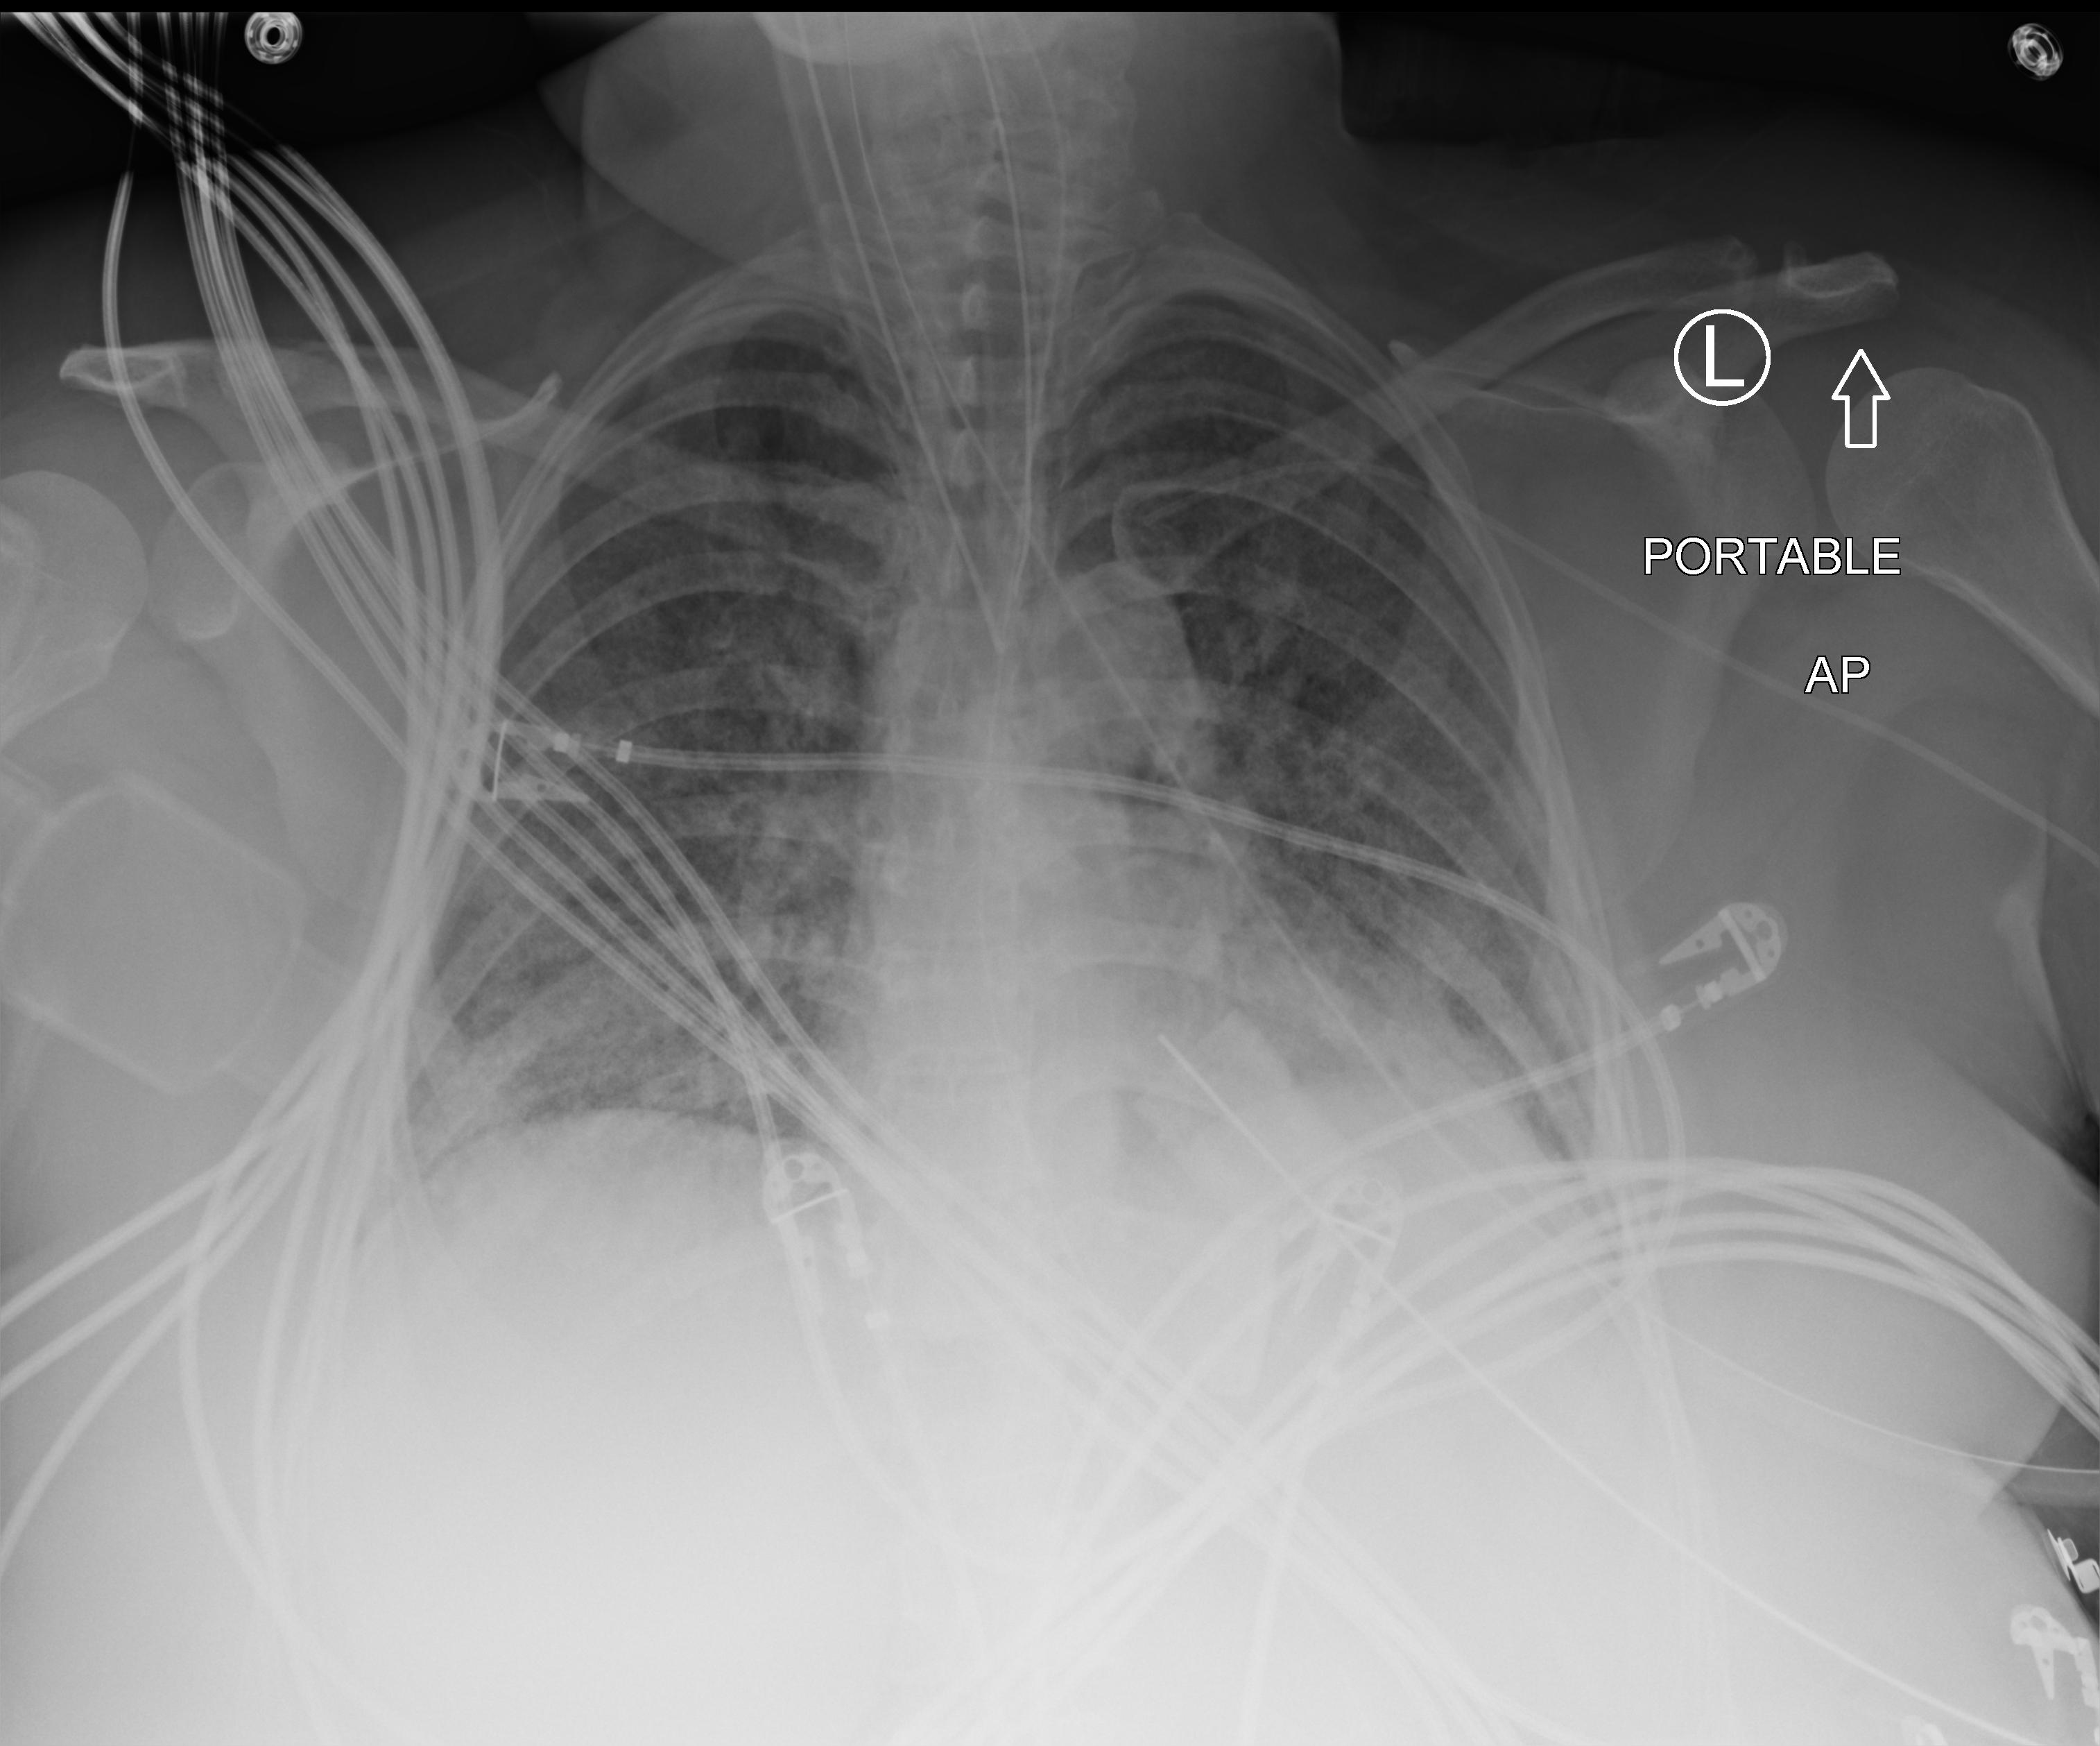
Bedside chest radiograph (computed radiography), anteroposterior (AP) projection. Patient hospitalised with COVID-19; female, aged 18–59 years.
Hospital-stay facts (about this admission, not read from this image; timing relative to this image not recorded):
- admitted to intensive care during this hospital stay: yes
- mechanically ventilated during this hospital stay: yes